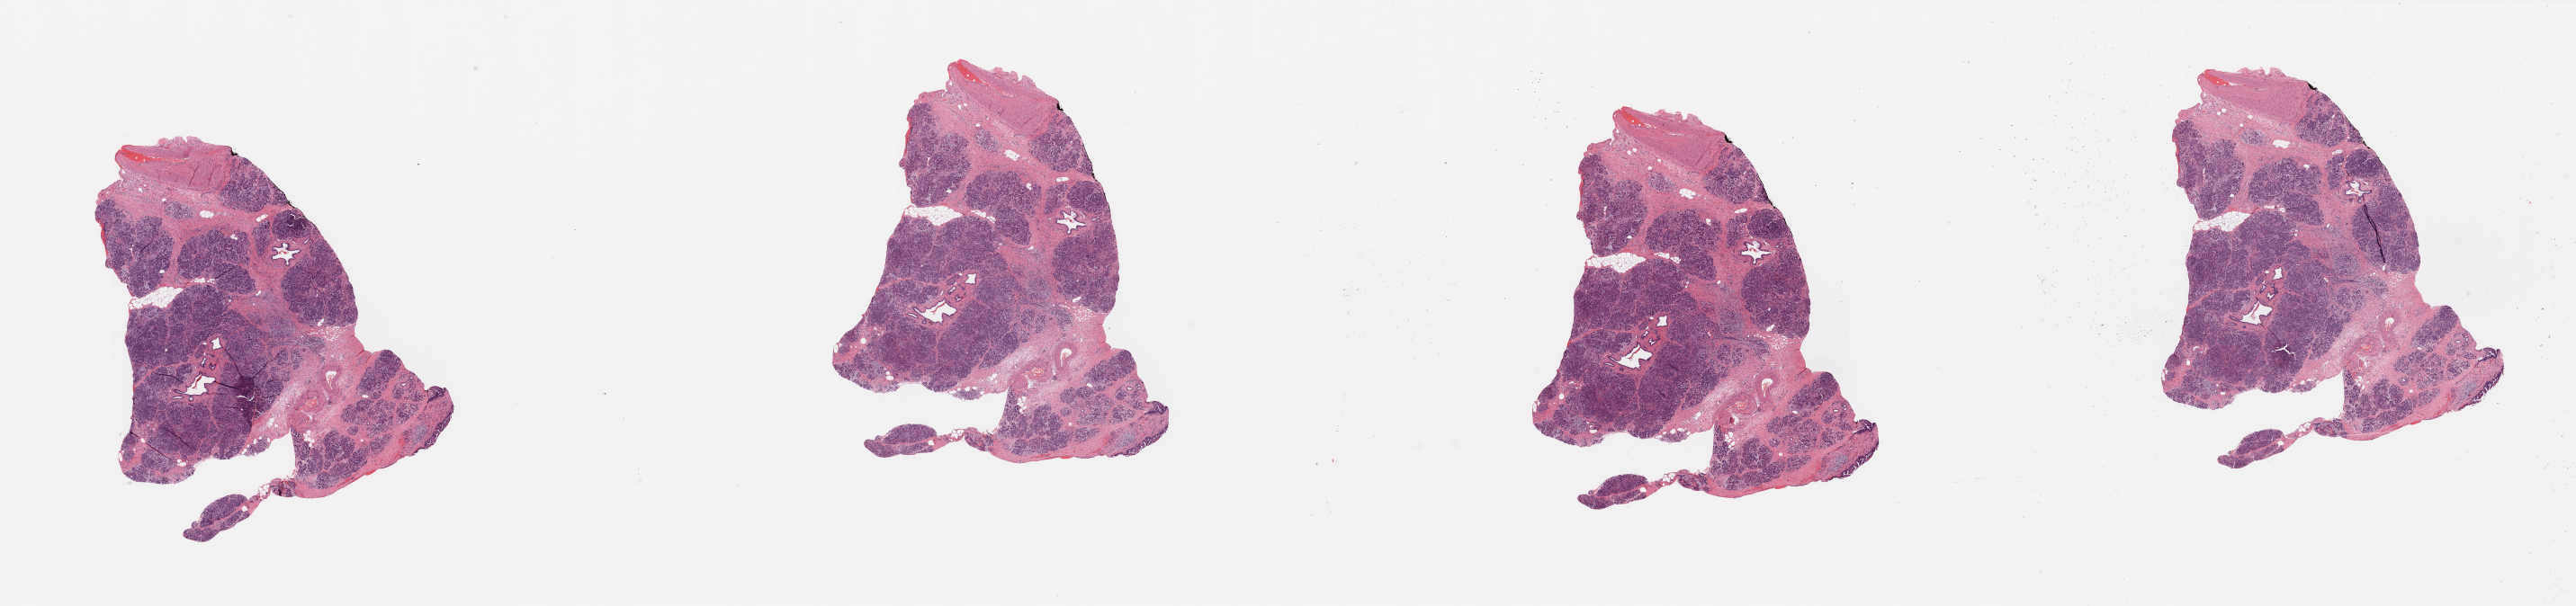
Digitized Hematoxylin and eosin (H&E) stained tissue section (whole slide) — shown as a low-resolution overview of the whole scanned area (about 45.3 x 10.7 mm, from a 20x scan); pancreas, tumour tissue. Patient: male, age 80 years. Histologic grade: G2 (moderately differentiated).
Diagnosis: Infiltrating duct carcinoma, NOS. AJCC pathologic stage: IIB. Primary tumour site (as recorded): head.